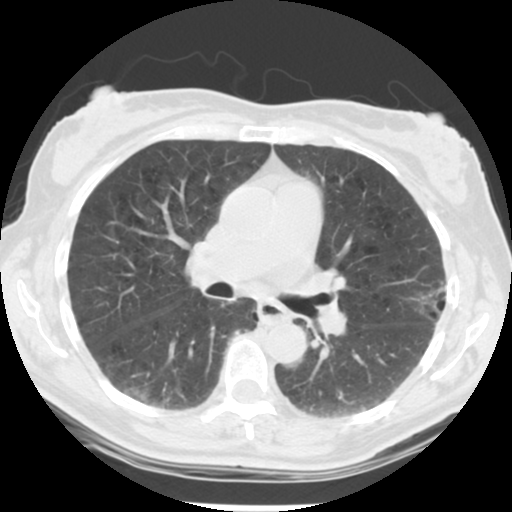
Low-dose screening chest CT, one axial slice; position 126 of 223 along the scan axis; reconstruction kernel STANDARD; 120 kVp; lung window (W 1500 / L -600 HU); 512 × 512 image matrix, field of view 302 × 302 mm.
Outlined on this slice (expert manual segmentation):
- lesion 1 (tumor, upper lobe of left lung): bounding box [x1, y1, x2, y2] px = [416, 281, 447, 314]